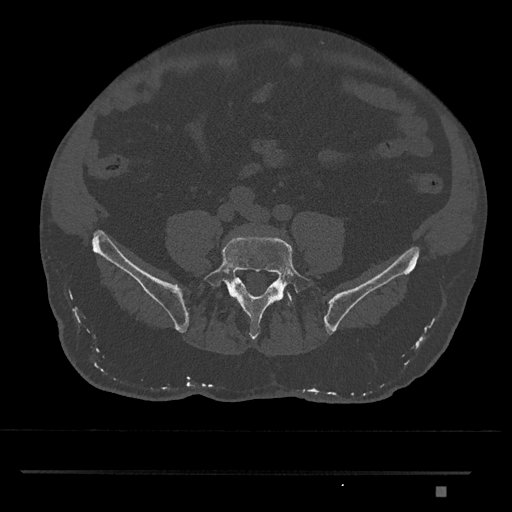
CT including the spine, one axial slice; slice 559 of 1134 in the series (ordered by position); reconstruction kernel Br40s/3; bone window (W 1800 / L 400 HU); 0.5 mm slice thickness; 512 × 512 image matrix, field of view 429 × 429 mm. Male patient, age 65 years. Case-level facts recorded for this patient, not image findings: primary cancer: prostate.
Structures marked on this image (semi-automatic segmentation, software-assisted and operator-edited):
- L5 vertebra: bounding box [x1, y1, x2, y2] px = [203, 236, 316, 340]